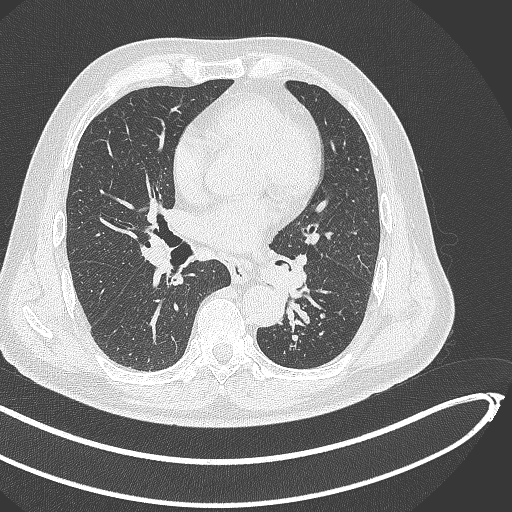
Chest CT, one axial slice; slice 240 of 468 in the series (ordered by position); 120 kVp; lung window (W 1500 / L -600 HU); 1 mm slice thickness; 512 × 512 image matrix. Patient: male, 64 years. Case-level facts recorded for this patient, not image findings: clinical TNM (as recorded): T1c N0 M0; histopathological grade: G2.
Annotated regions visible in this slice (bounding box drawn by a radiologist):
- lung tumour (recorded histology: squamous cell carcinoma): bounding box <255,250,300,307> (left, top, right, bottom; pixels)